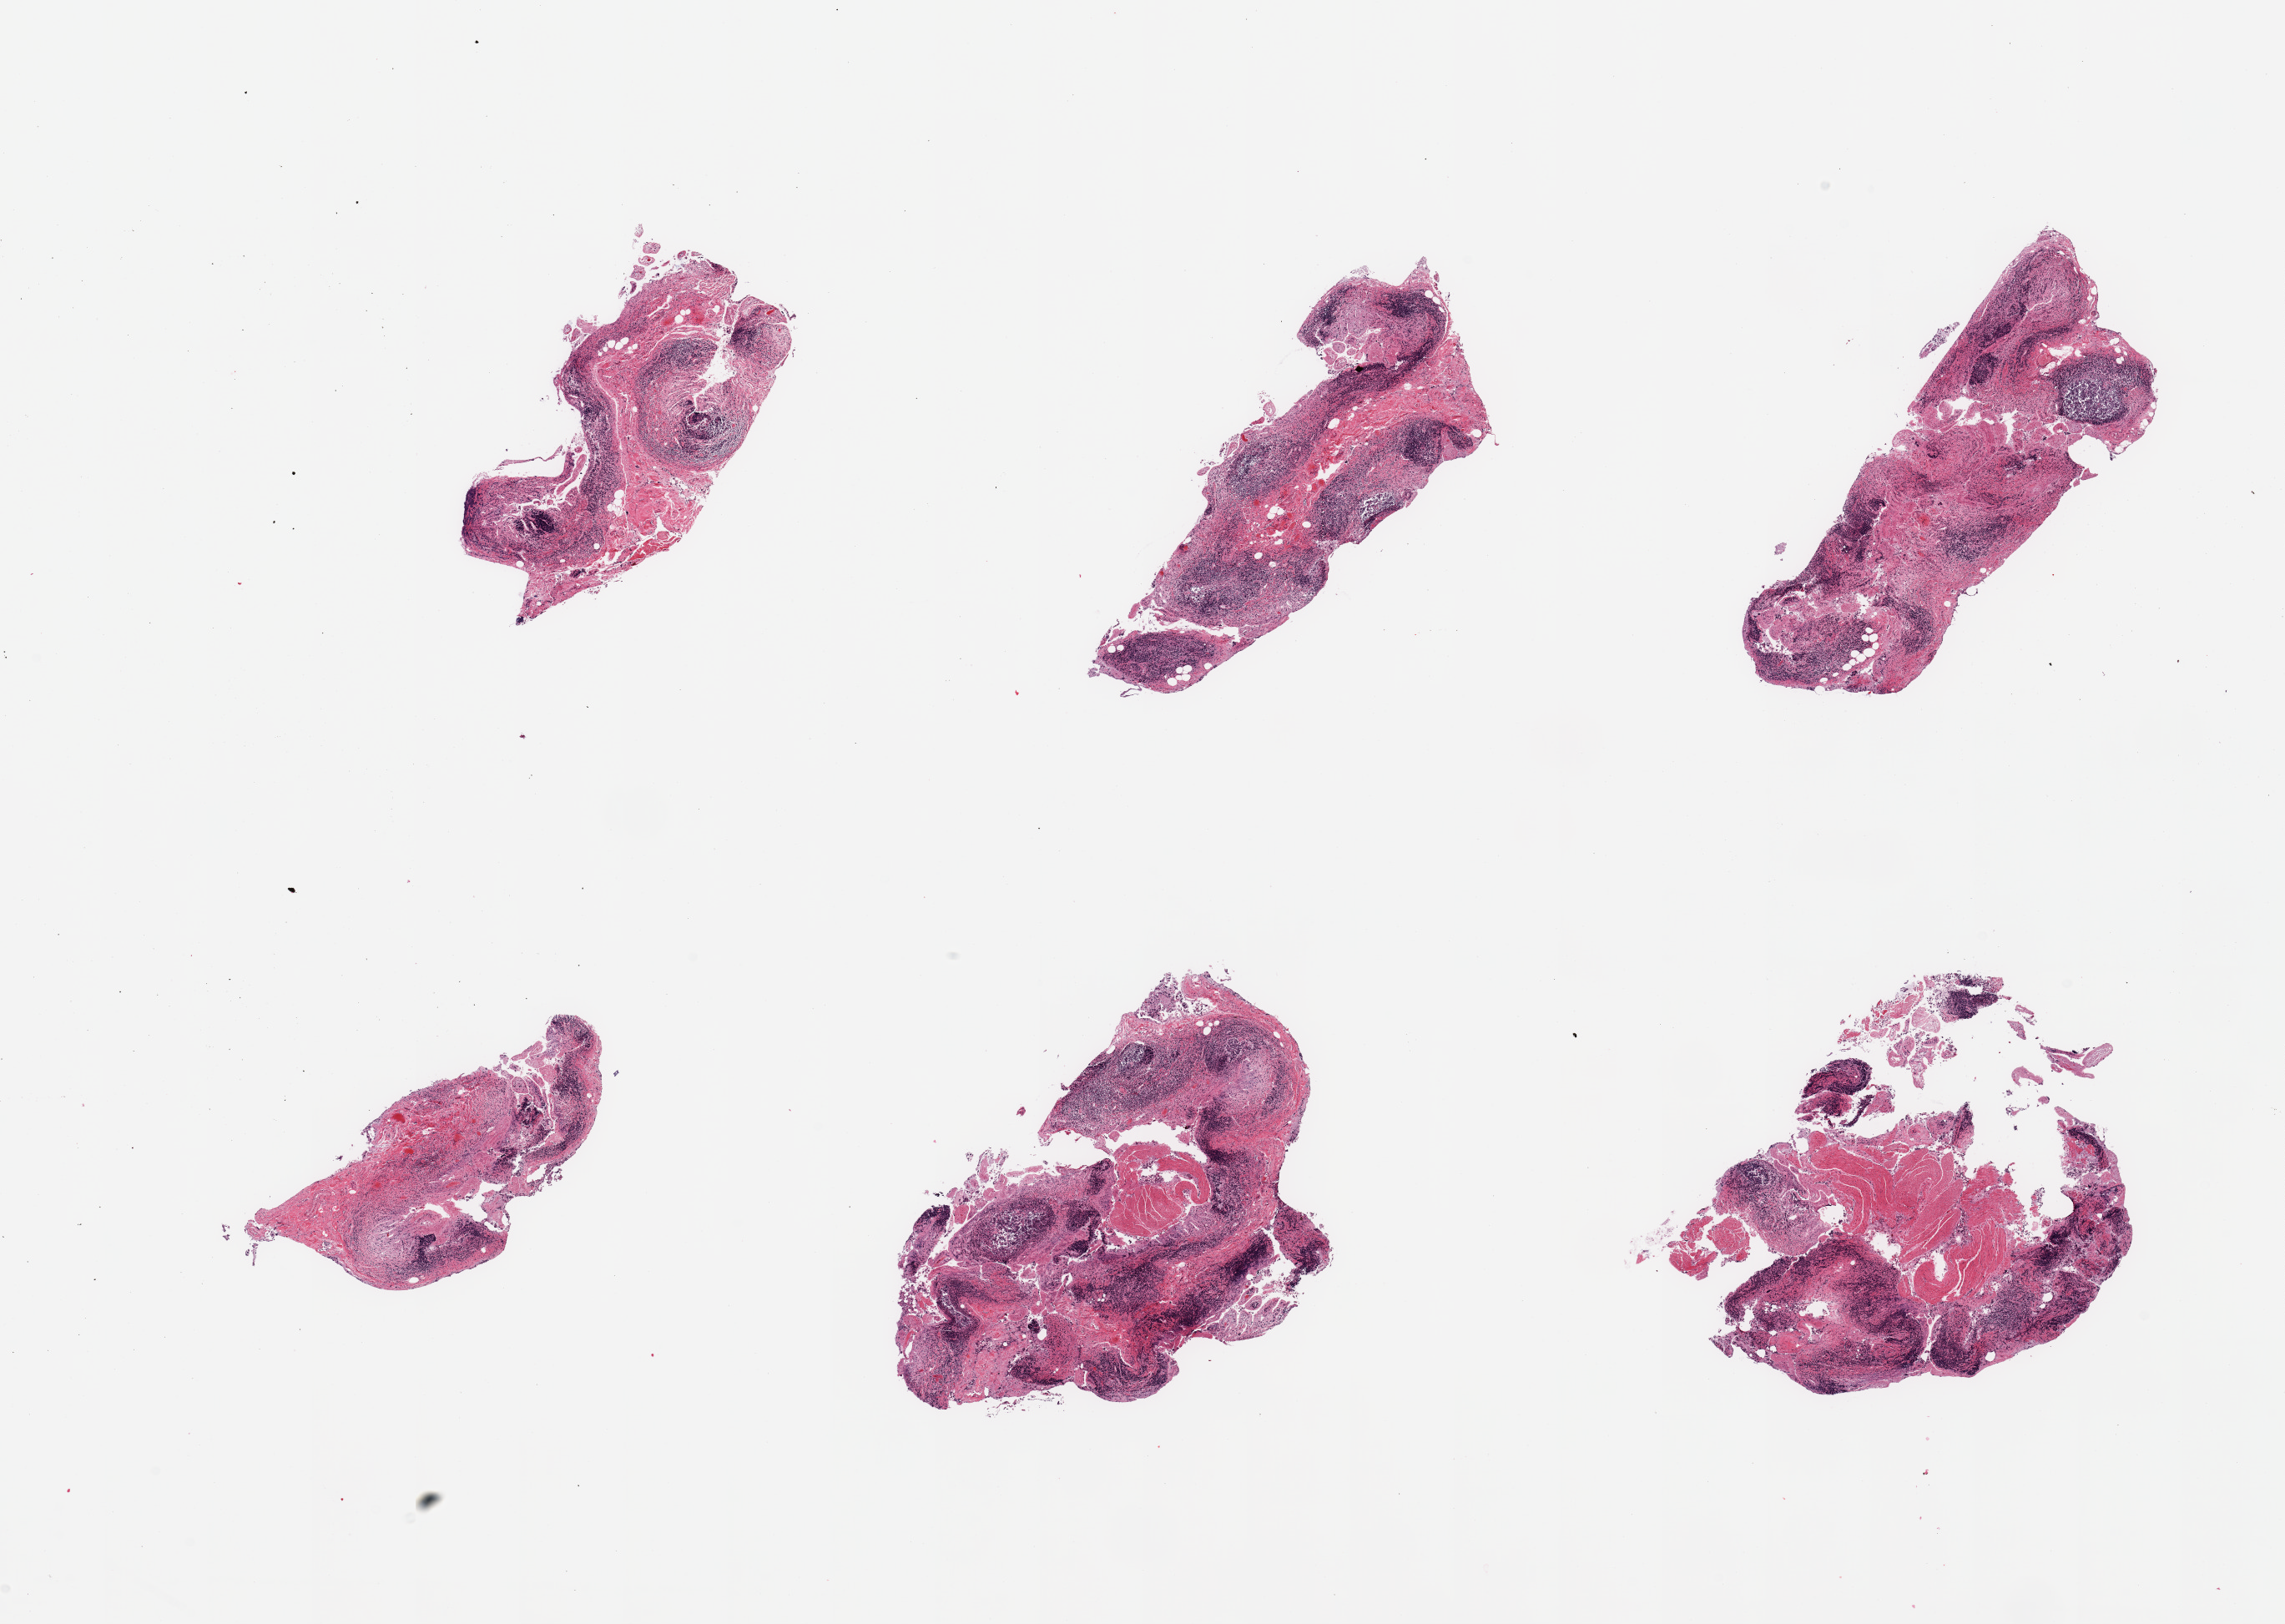
Digitized hematoxylin and eosin (H&E)-stained section, brightfield, whole scanned area (about 21.7 x 15.4 mm) shown as a low-resolution overview, PAXgene-fixed, paraffin-embedded tissue, section of ileum (target tissue), donor tissue sample.
• reviewer comment on this tissue sample: 6 pieces; well dissected lymphoid tissue, but autolysis and admixture with adjacent muscle limit usefulness